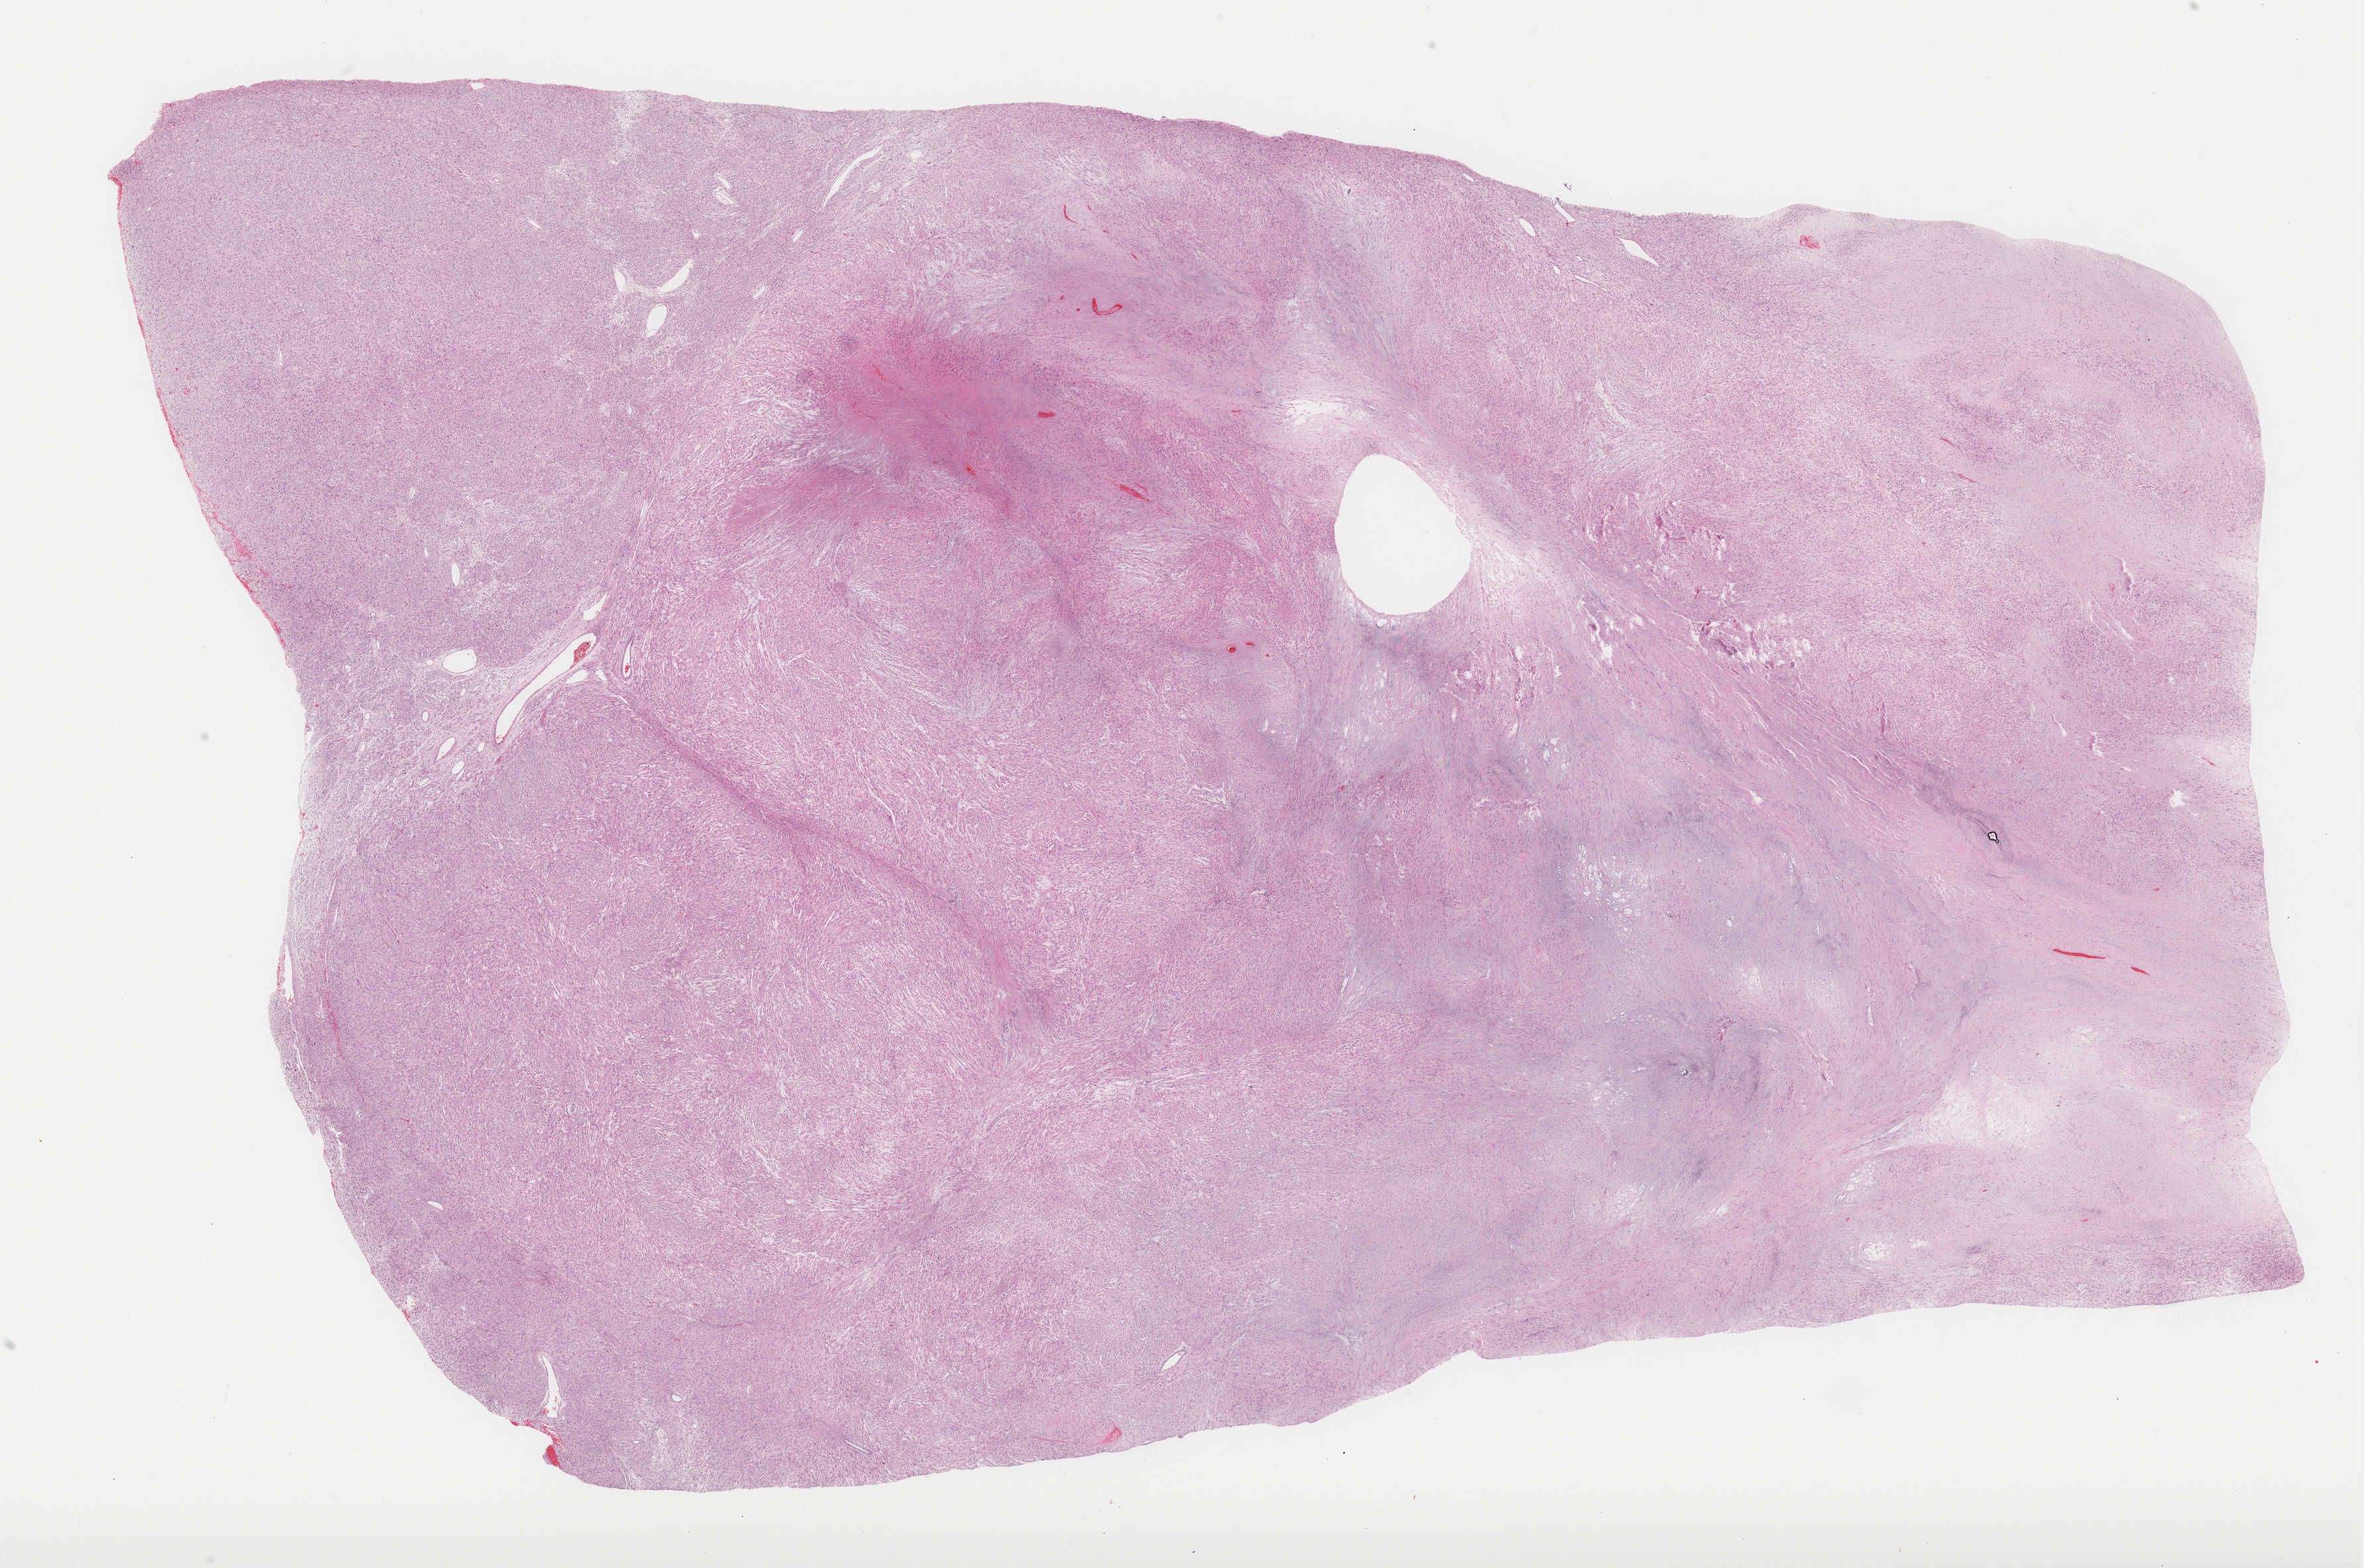
Whole-slide histology image, H&E — shown as a low-resolution overview of the whole scanned area (about 28.5 x 18.9 mm), FFPE section, retroperitoneum and peritoneum, primary tumour sample. Female patient; age at initial diagnosis 53 years.
Diagnosis: Leiomyosarcoma, NOS (retroperitoneum).